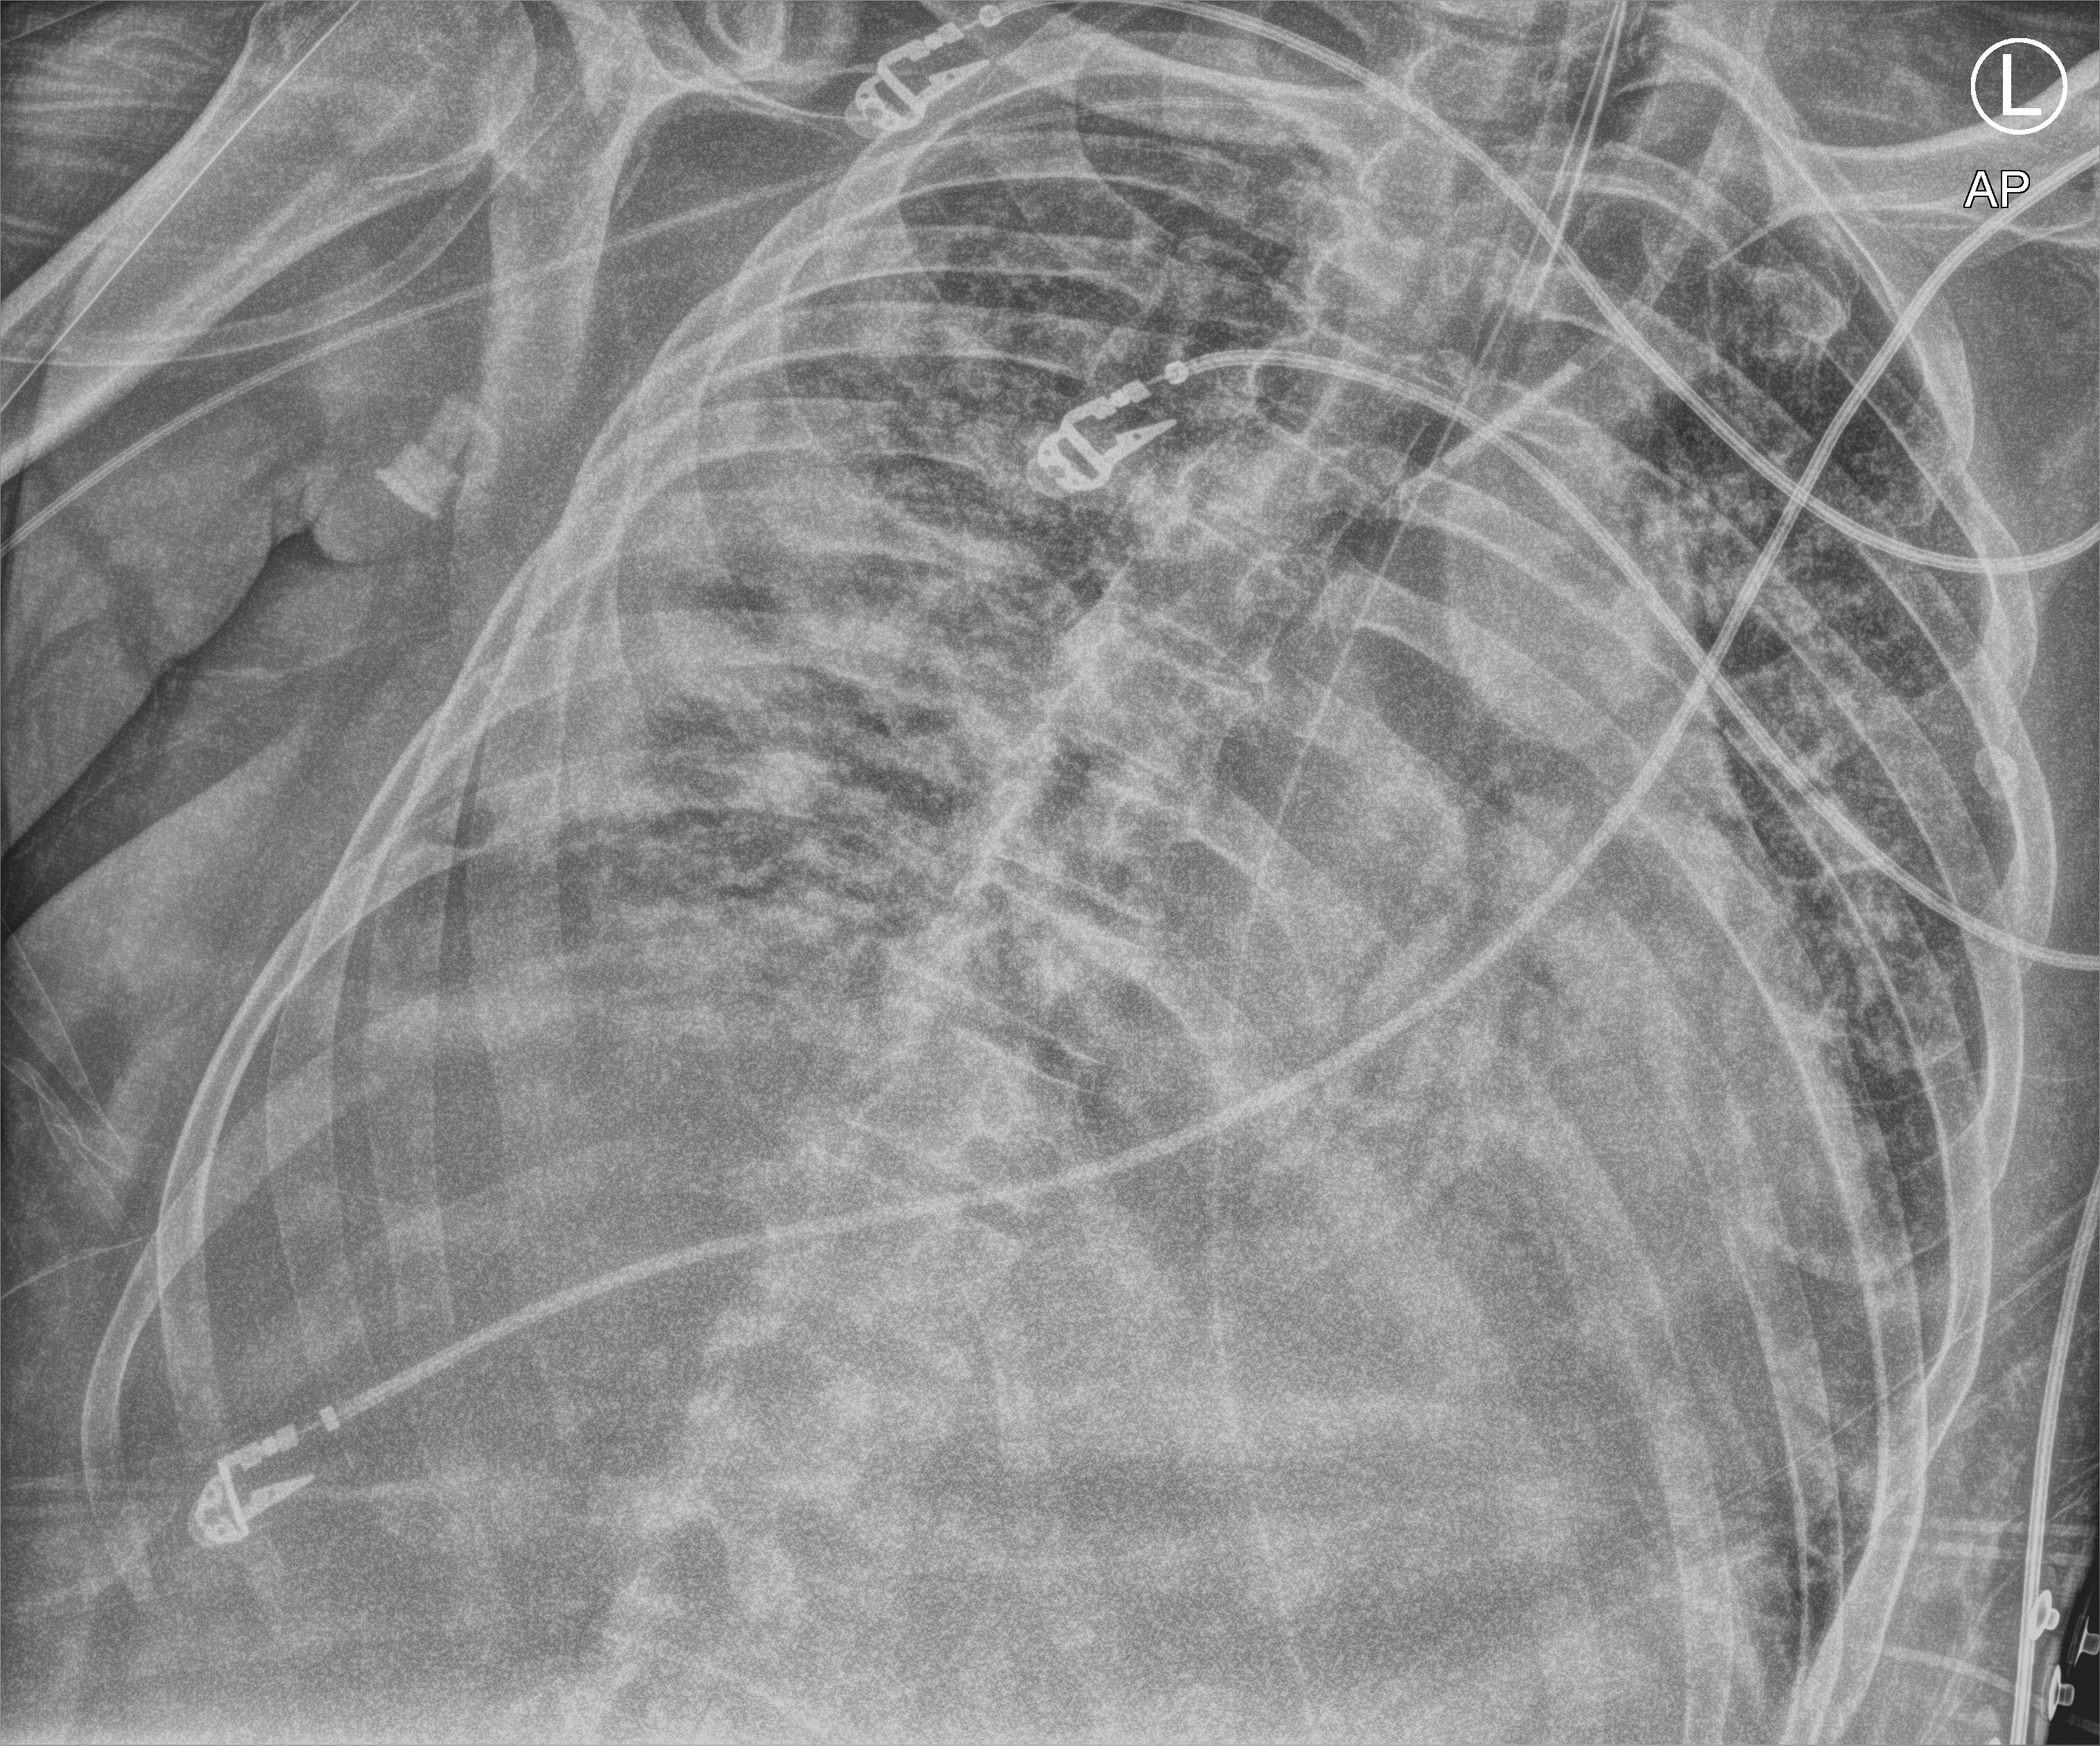
Chest X-ray (portable); anteroposterior (AP) projection. Patient hospitalised with COVID-19; male, aged 18–59 years.
From the hospital-stay record, not from the radiograph (when in the stay this image was taken is not recorded):
- COPD (admission record): no
- admitted to intensive care during this hospital stay: yes
- other chronic lung disease (admission record): no